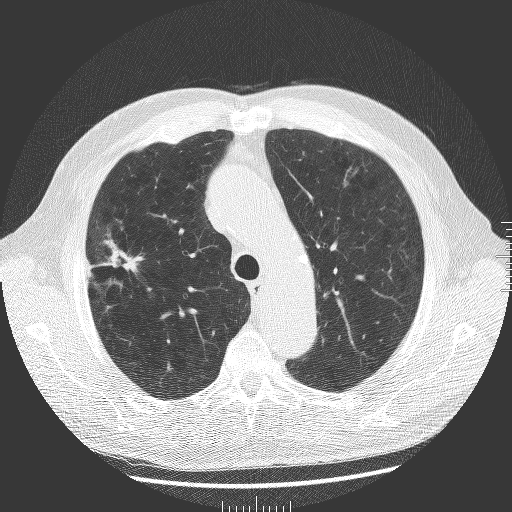
Low-dose screening chest CT, one axial slice. Slice 139 of 181 in the series (ordered by position). Lung window (W 1500 / L -600 HU). 512 × 512 image matrix, field of view 380 × 380 mm.
Structures marked on this image (outlined manually by an expert reader):
- lesion 1 (tumor, upper lobe of right lung): bounding box (x1, y1, x2, y2) in pixels: (105, 239, 143, 273)